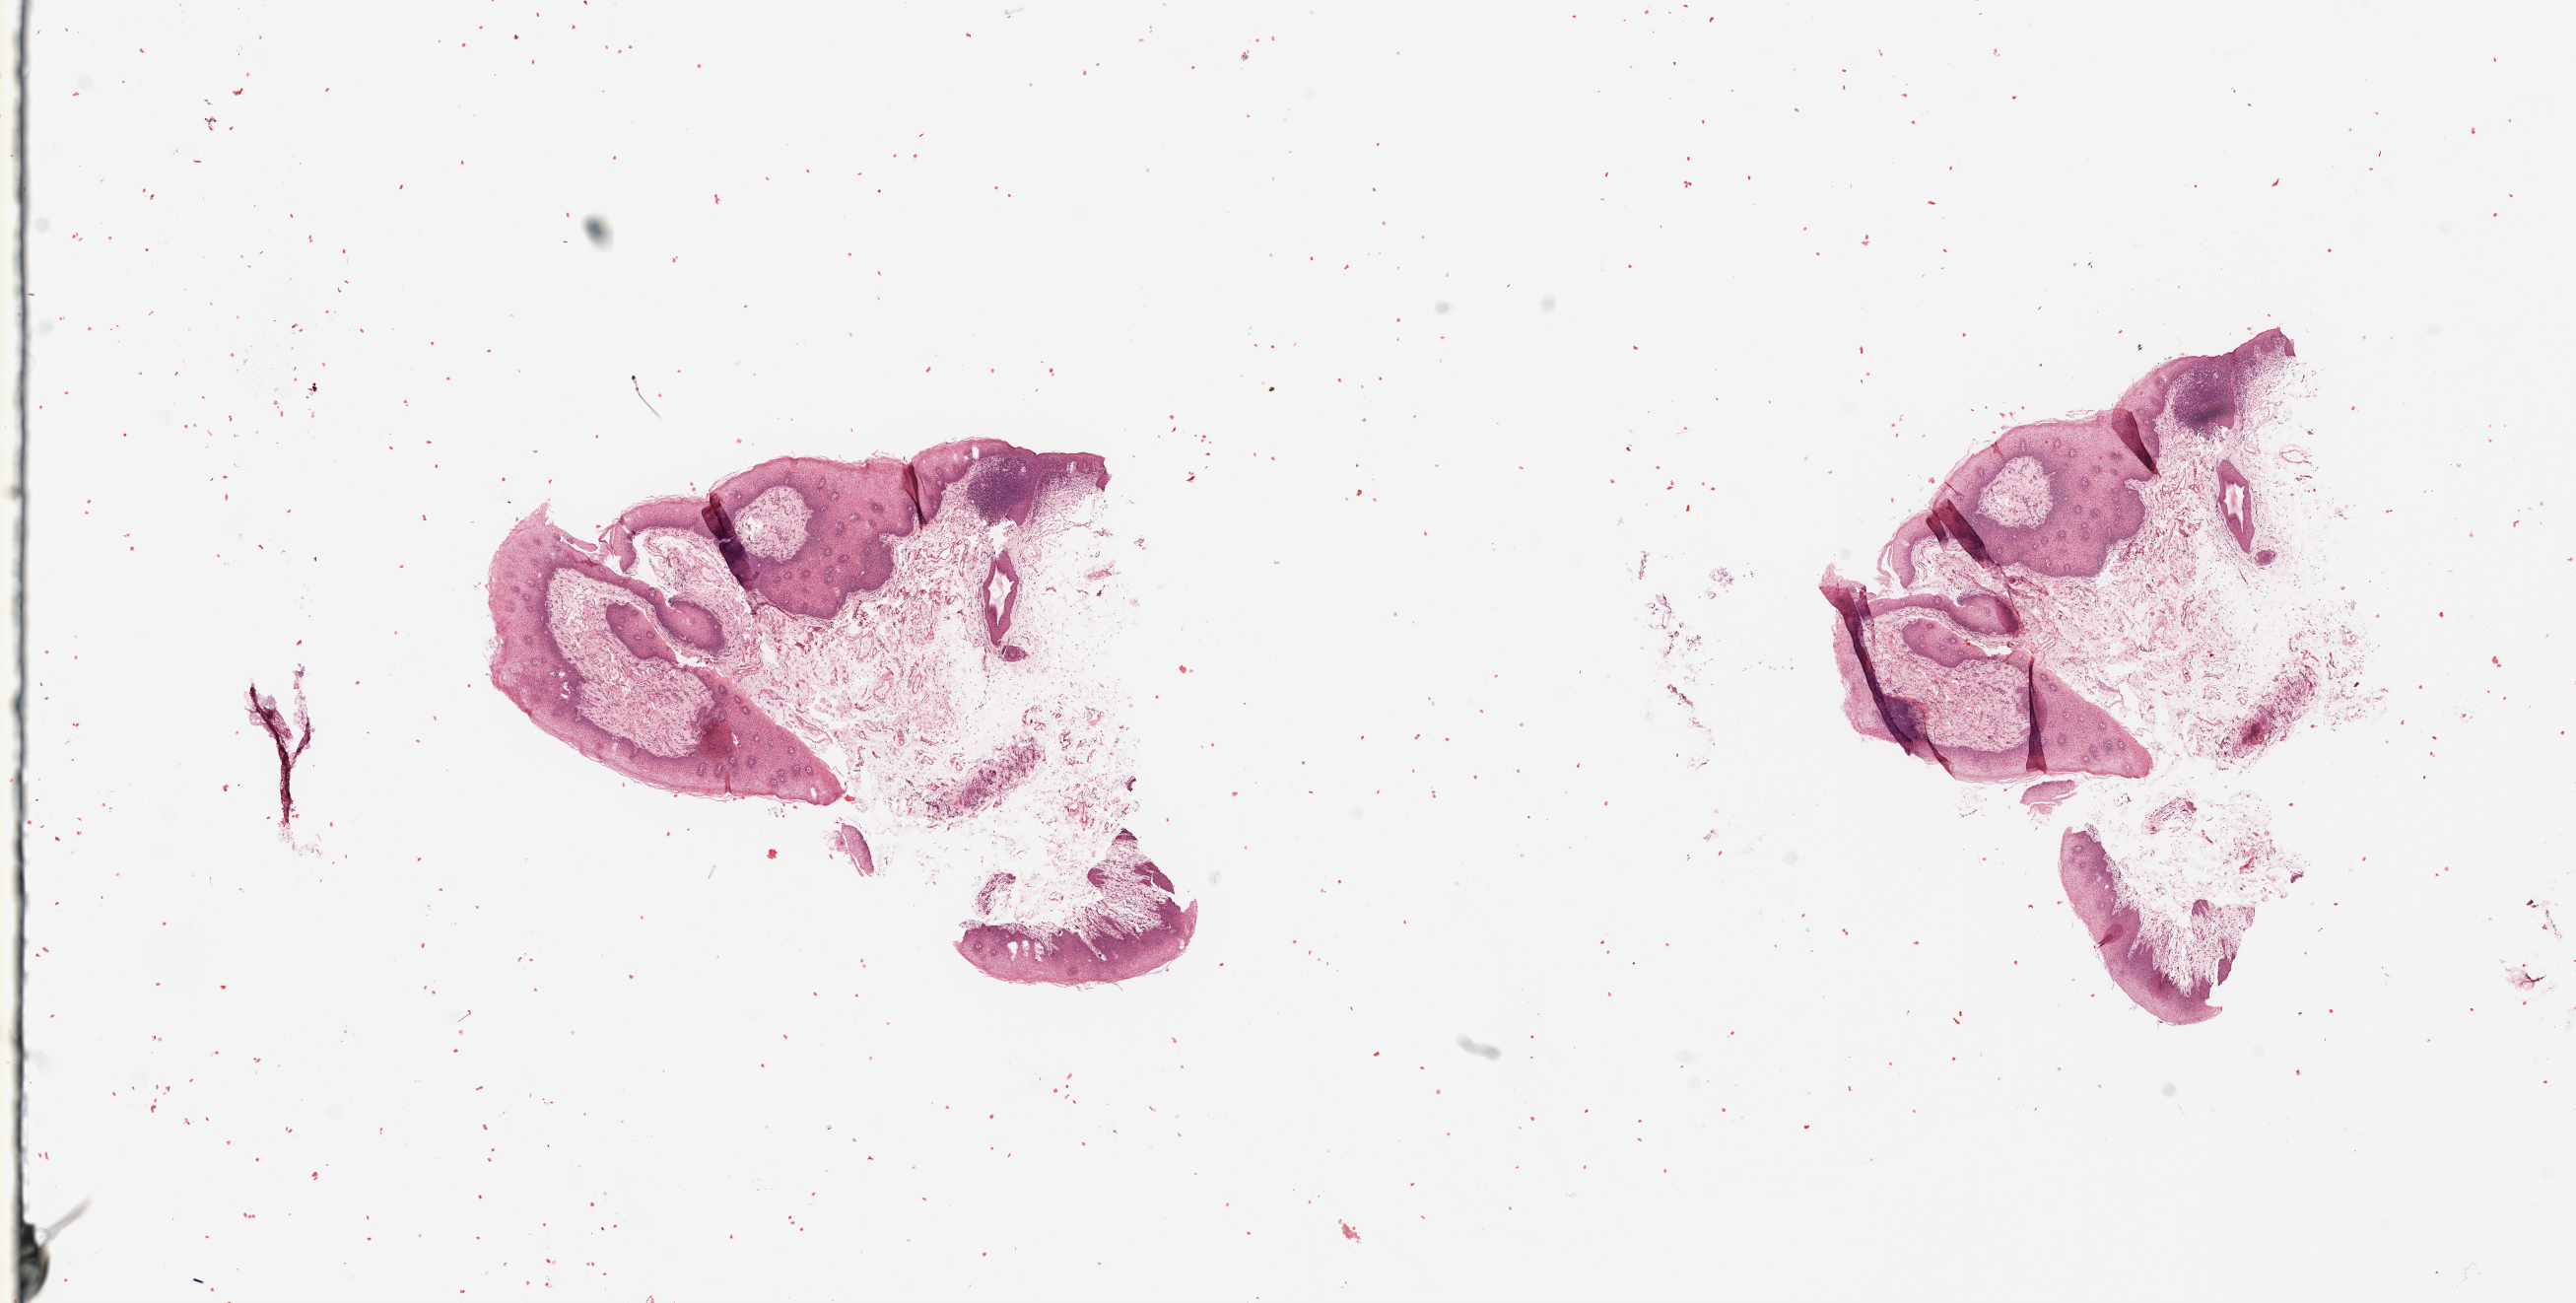
Hematoxylin and eosin (H&E) stained whole-slide image — shown as a low-resolution overview of the whole scanned area (about 20.7 x 10.5 mm, acquisition: 20x scan), normal (non-tumour) tissue sample, sampled site: larynx. Patient: male, age 62 years.
This section: normal (non-tumour) tissue from the same patient. Patient diagnosis: Squamous cell carcinoma, NOS (larynx, NOS).